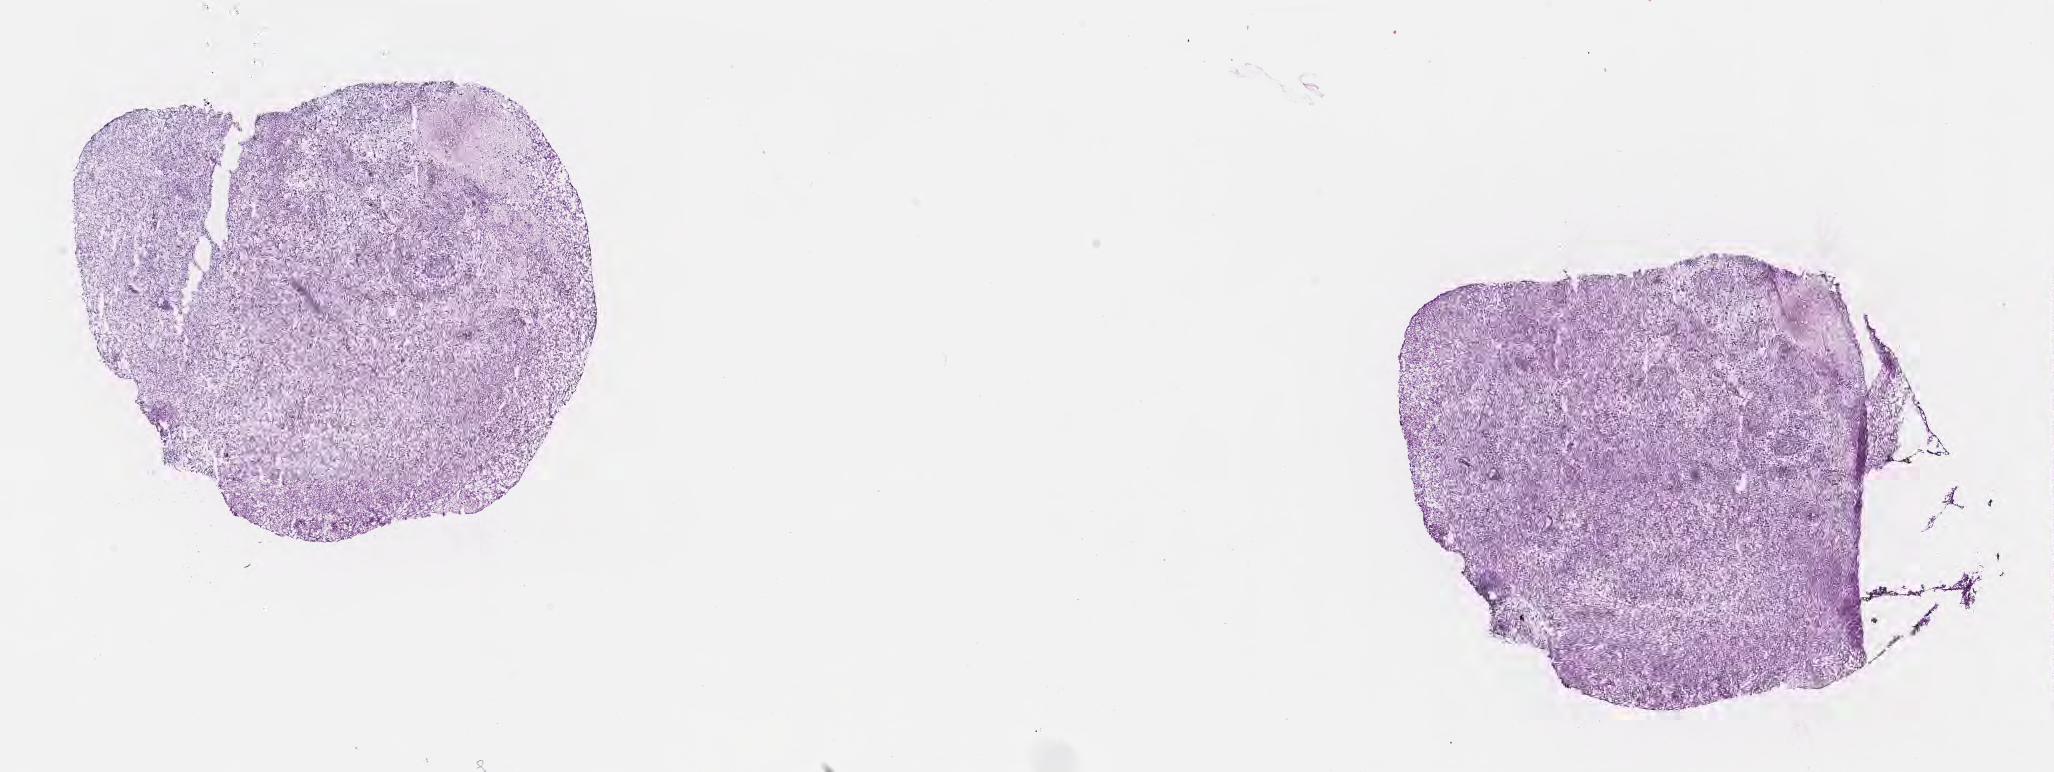
Hematoxylin and eosin (H&E) whole-slide image, low-resolution overview of the scanned area, about 16.6 x 6.2 mm; frozen section; specimen: primary tumor; site: brain. Female patient; age at initial diagnosis 56 years. Slide review estimates, as recorded: tumor cells 86%, tumor nuclei 93%, stromal cells 7%, necrosis 1%, normal cells 6%. Inflammatory infiltration, as recorded: lymphocyte infiltration 0%, monocyte infiltration 0%, neutrophil infiltration 0%.
Histologic diagnosis: Glioblastoma, NOS. Section: bottom of the tissue portion.